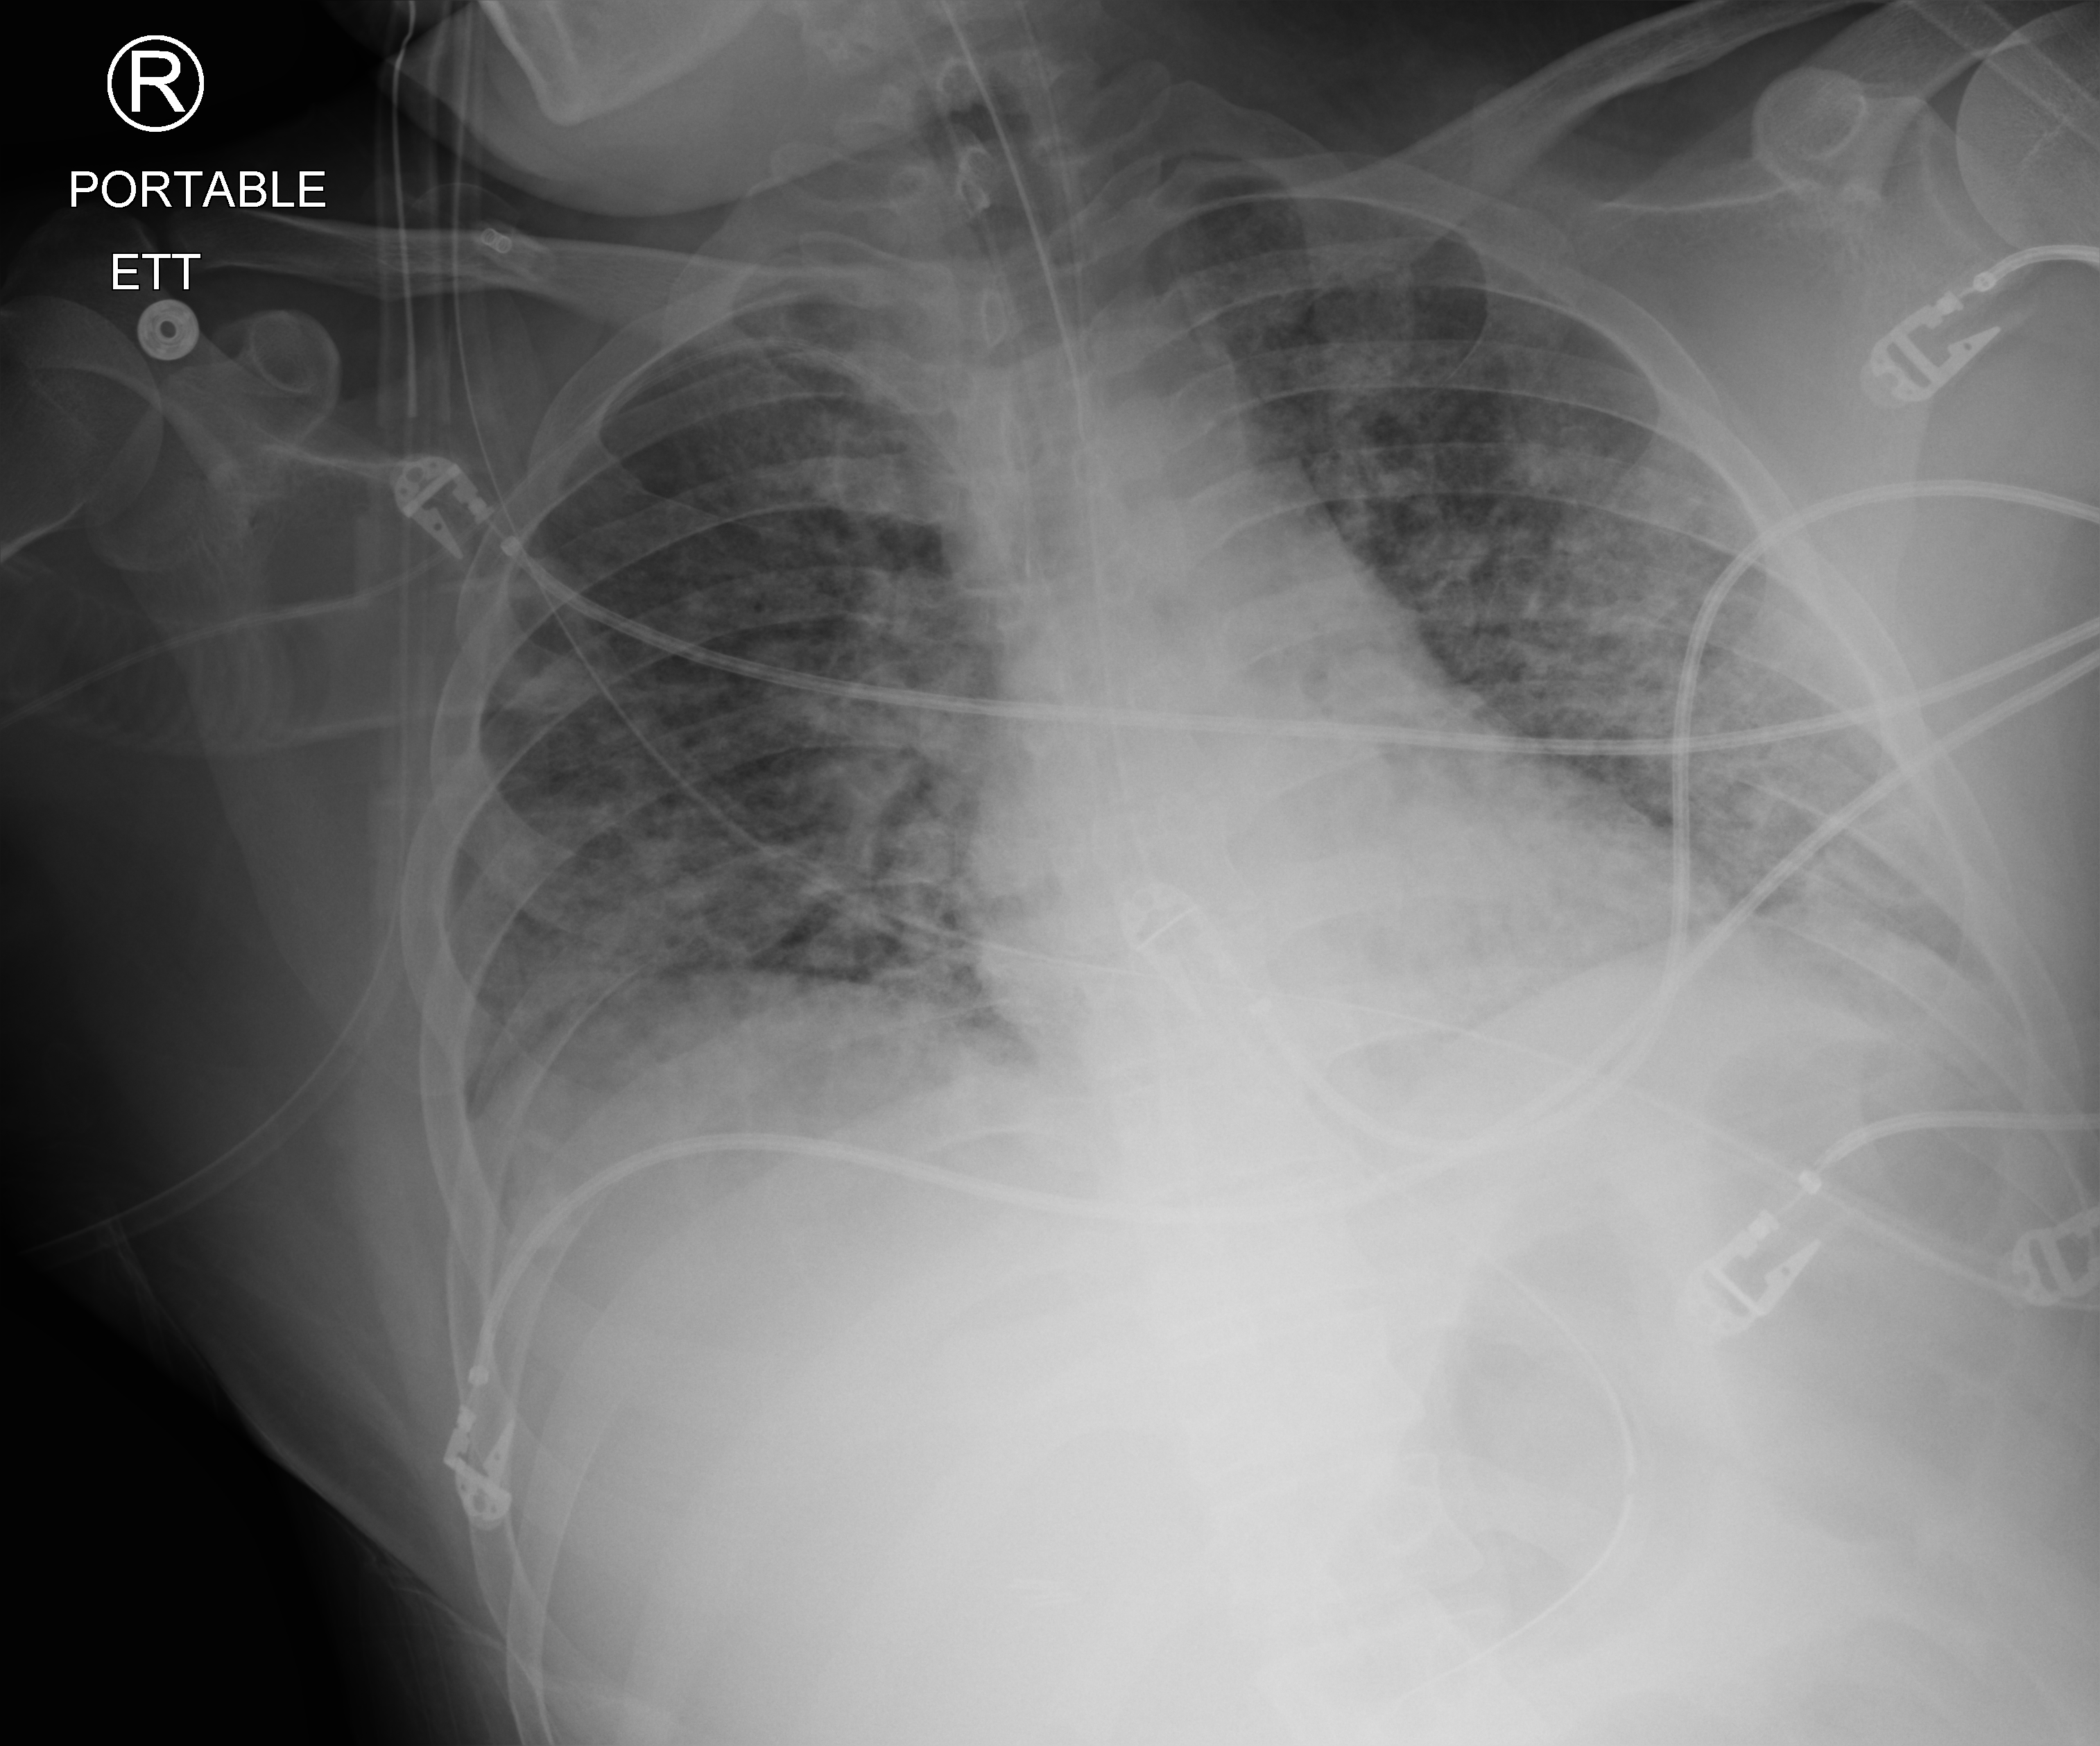
Portable chest radiograph, anteroposterior (AP) projection. Patient hospitalised with COVID-19; male, aged 18–59 years.
Admission-level facts for this patient (not findings on this image; timing relative to this image not recorded): diabetes (admission record): yes; mechanically ventilated during this hospital stay: yes; hypertension (admission record): no.